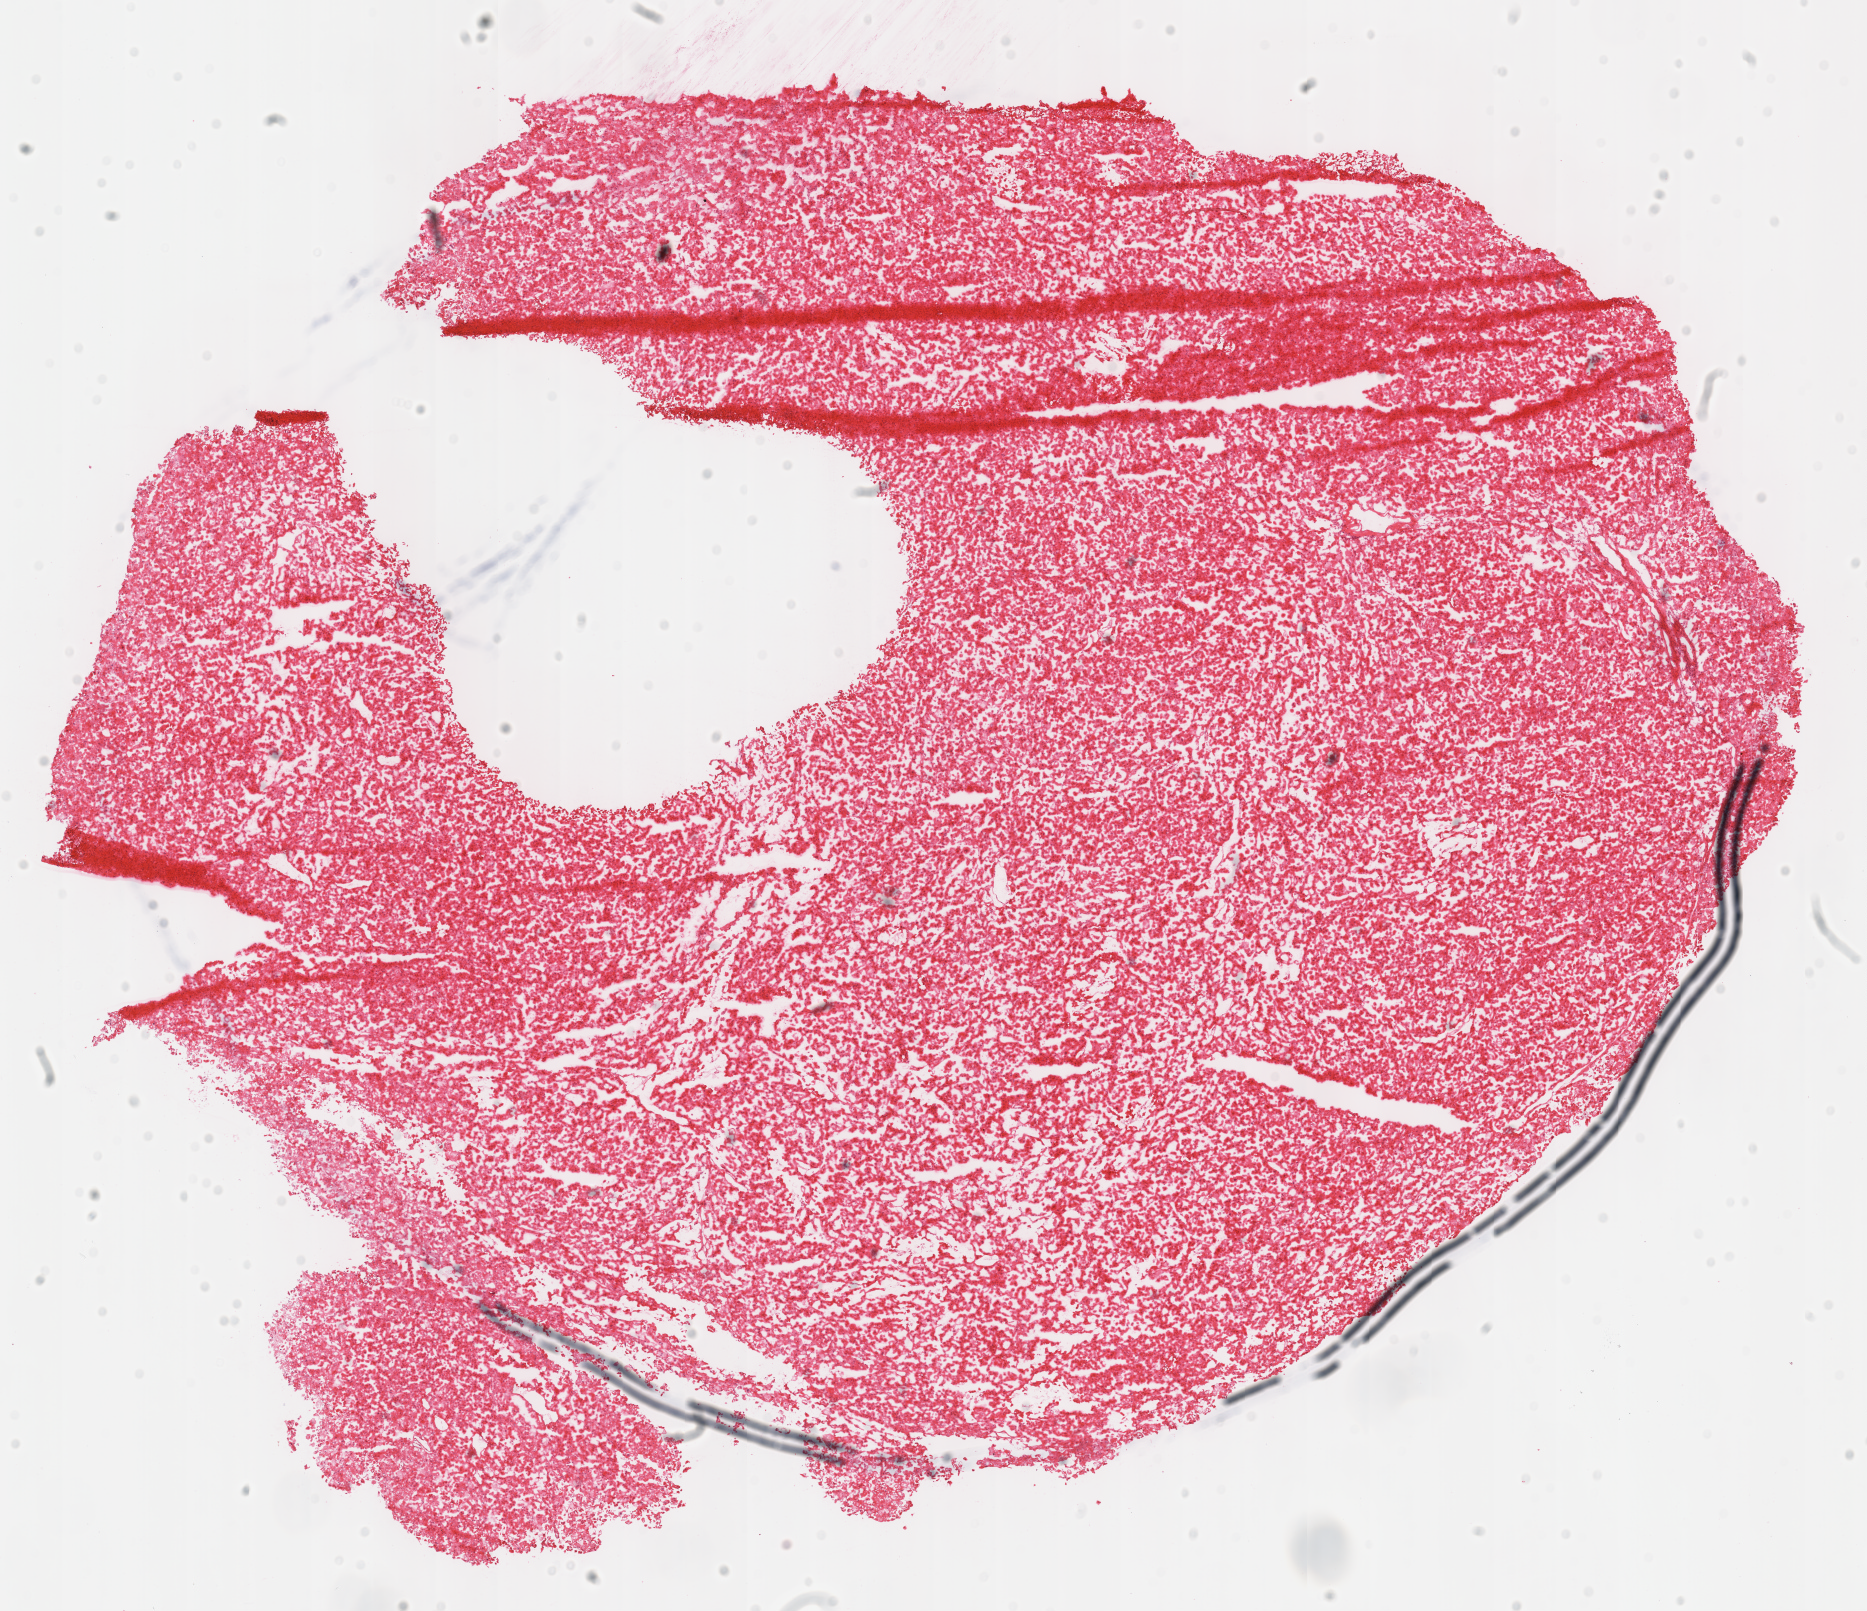
Whole-slide histology image, H&E — low-resolution overview of the scanned area, about 14.7 x 12.7 mm; frozen section; sample: primary tumour, kidney. Female patient; age at initial diagnosis 28 years. Composition of this section per pathologist review: tumour cells 100%, tumour nuclei 95%, normal cells 0%, stromal cells 0%, necrosis 0%. Infiltration values recorded for this section: lymphocyte infiltration 0%, monocyte infiltration 0%, neutrophil infiltration 0%.
* laterality: right
* AJCC pathologic stage: I (6th edition)
* TNM: T1a N0
* diagnosis: Renal cell carcinoma, chromophobe type